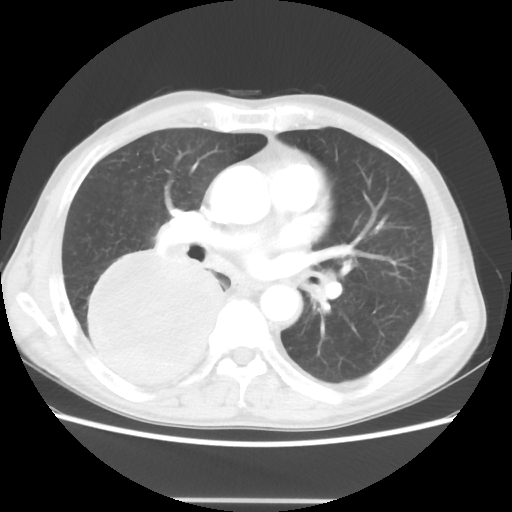
Chest CT, one axial slice. Position 24 of 48 along the scan axis. 100 kVp. Lung window (W 1500 / L -600 HU). 5 mm slice thickness. 512 × 512 image matrix. Patient: male, 66 years. Case-level facts recorded for this patient, not image findings: clinical TNM (as recorded): T4 N1 M1.
Annotated regions visible in this slice (rectangle marked by the reading radiologist):
- lung tumour (recorded histology: small cell carcinoma): box from (x=75, y=245) to (x=232, y=400) px